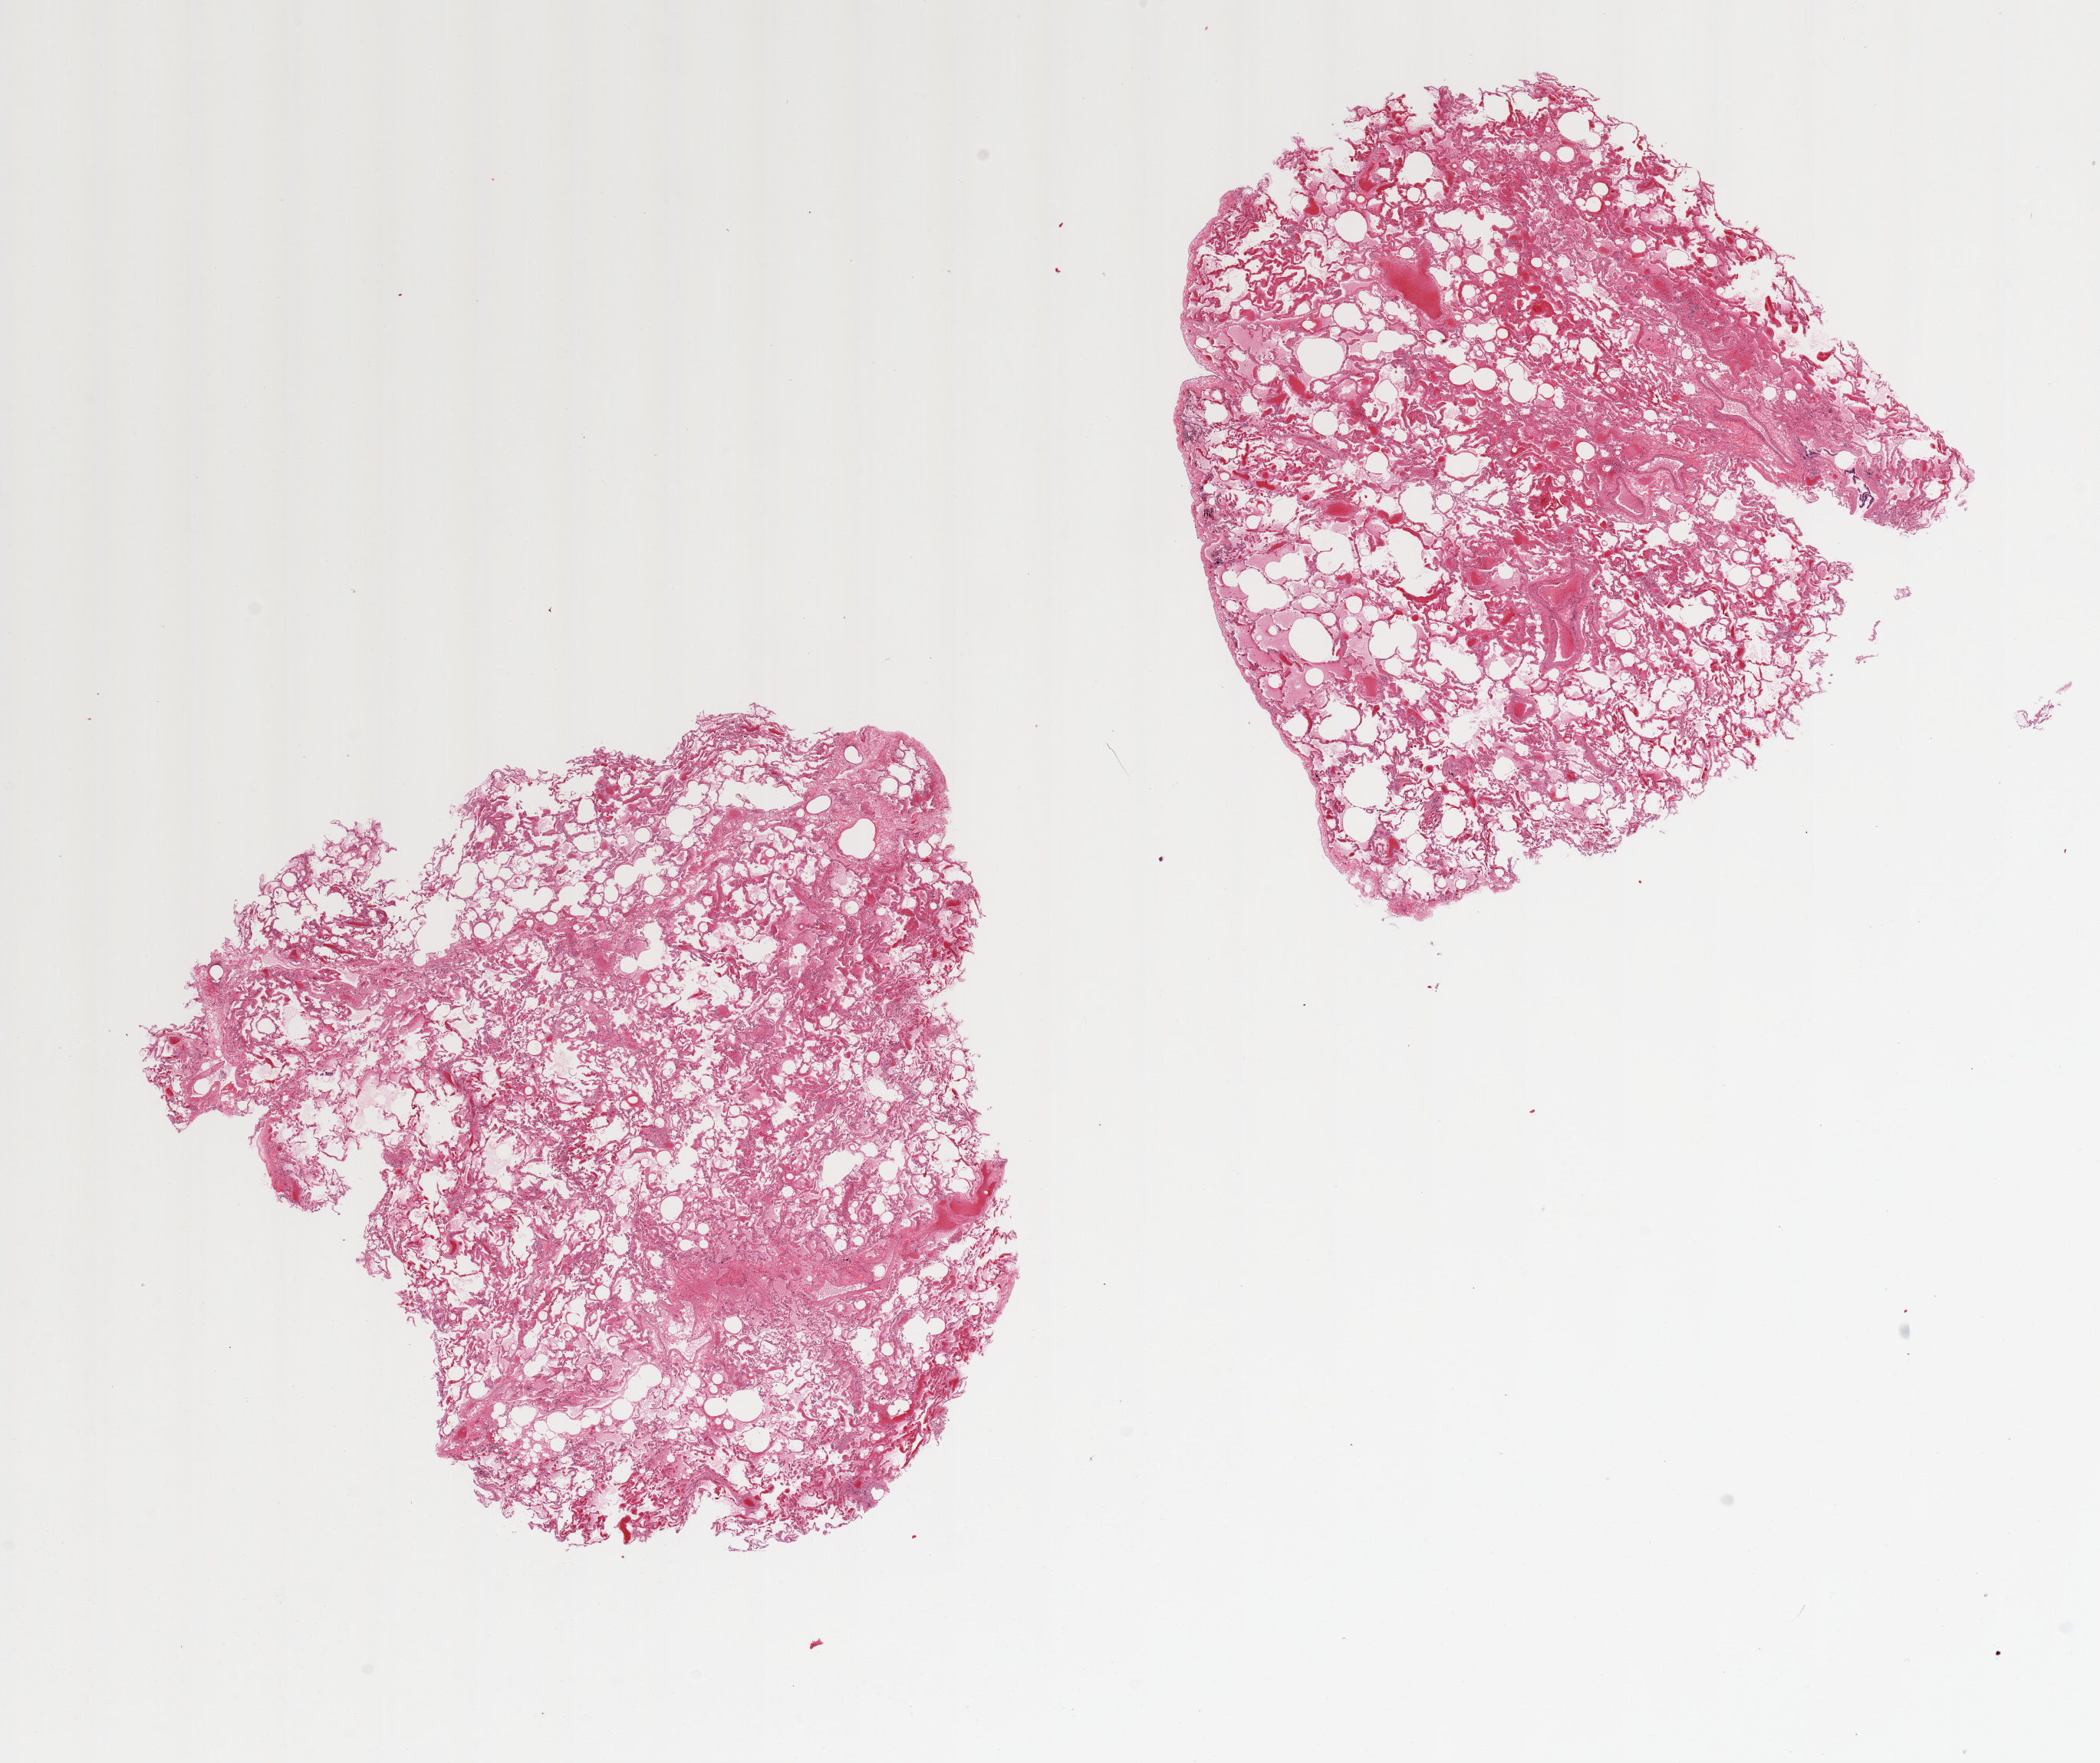
Whole-slide image, H&E stain — low-resolution overview of the scanned area, about 21.7 x 18.2 mm; PAXgene-fixed paraffin-embedded (PFPE) section; target tissue: lung; tissue donor sample. Donor sex: male.
- review note (as recorded): 2 pieces, moderate edema/congestion